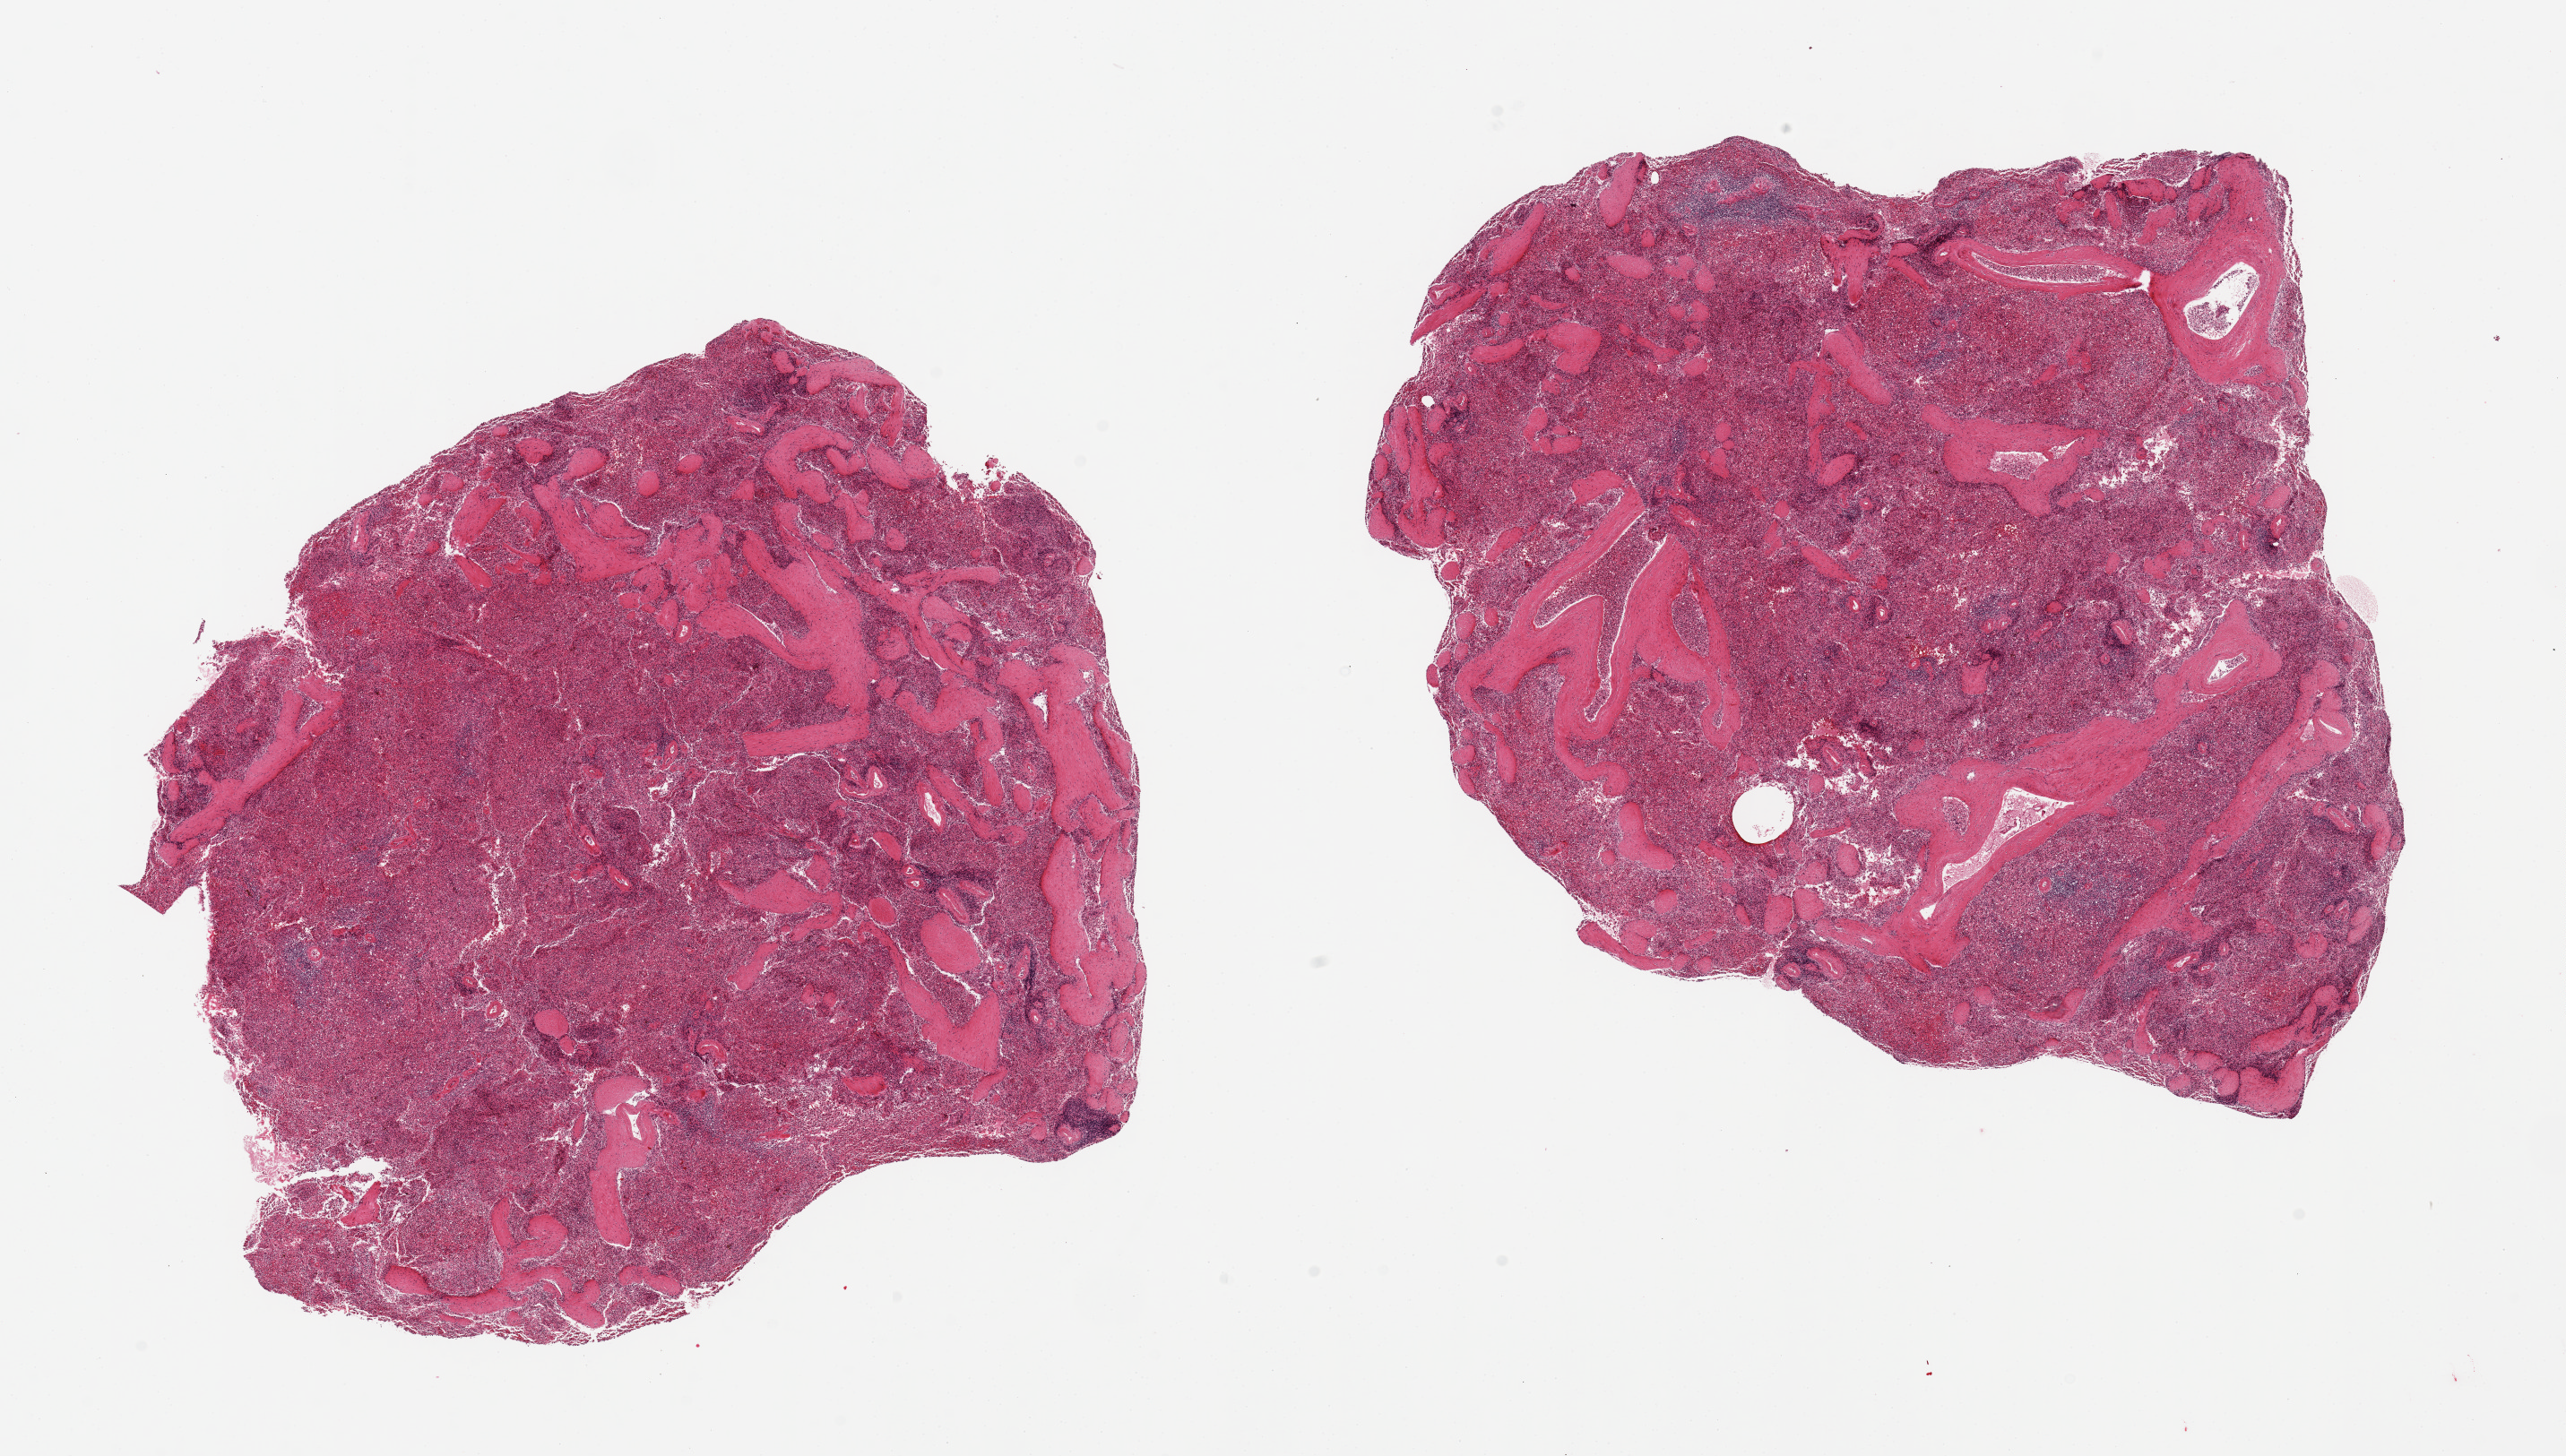
Whole-slide image, haematoxylin and eosin stain, brightfield — a low-resolution overview of the entire scanned area, about 22.6 x 12.9 mm. PAXgene-fixed, paraffin-embedded tissue. Target tissue: spleen. Tissue donor sample. Male donor.
Review note (as recorded): 2 pieces; expansion of red pulp, hemosiderin-laden macrophages.